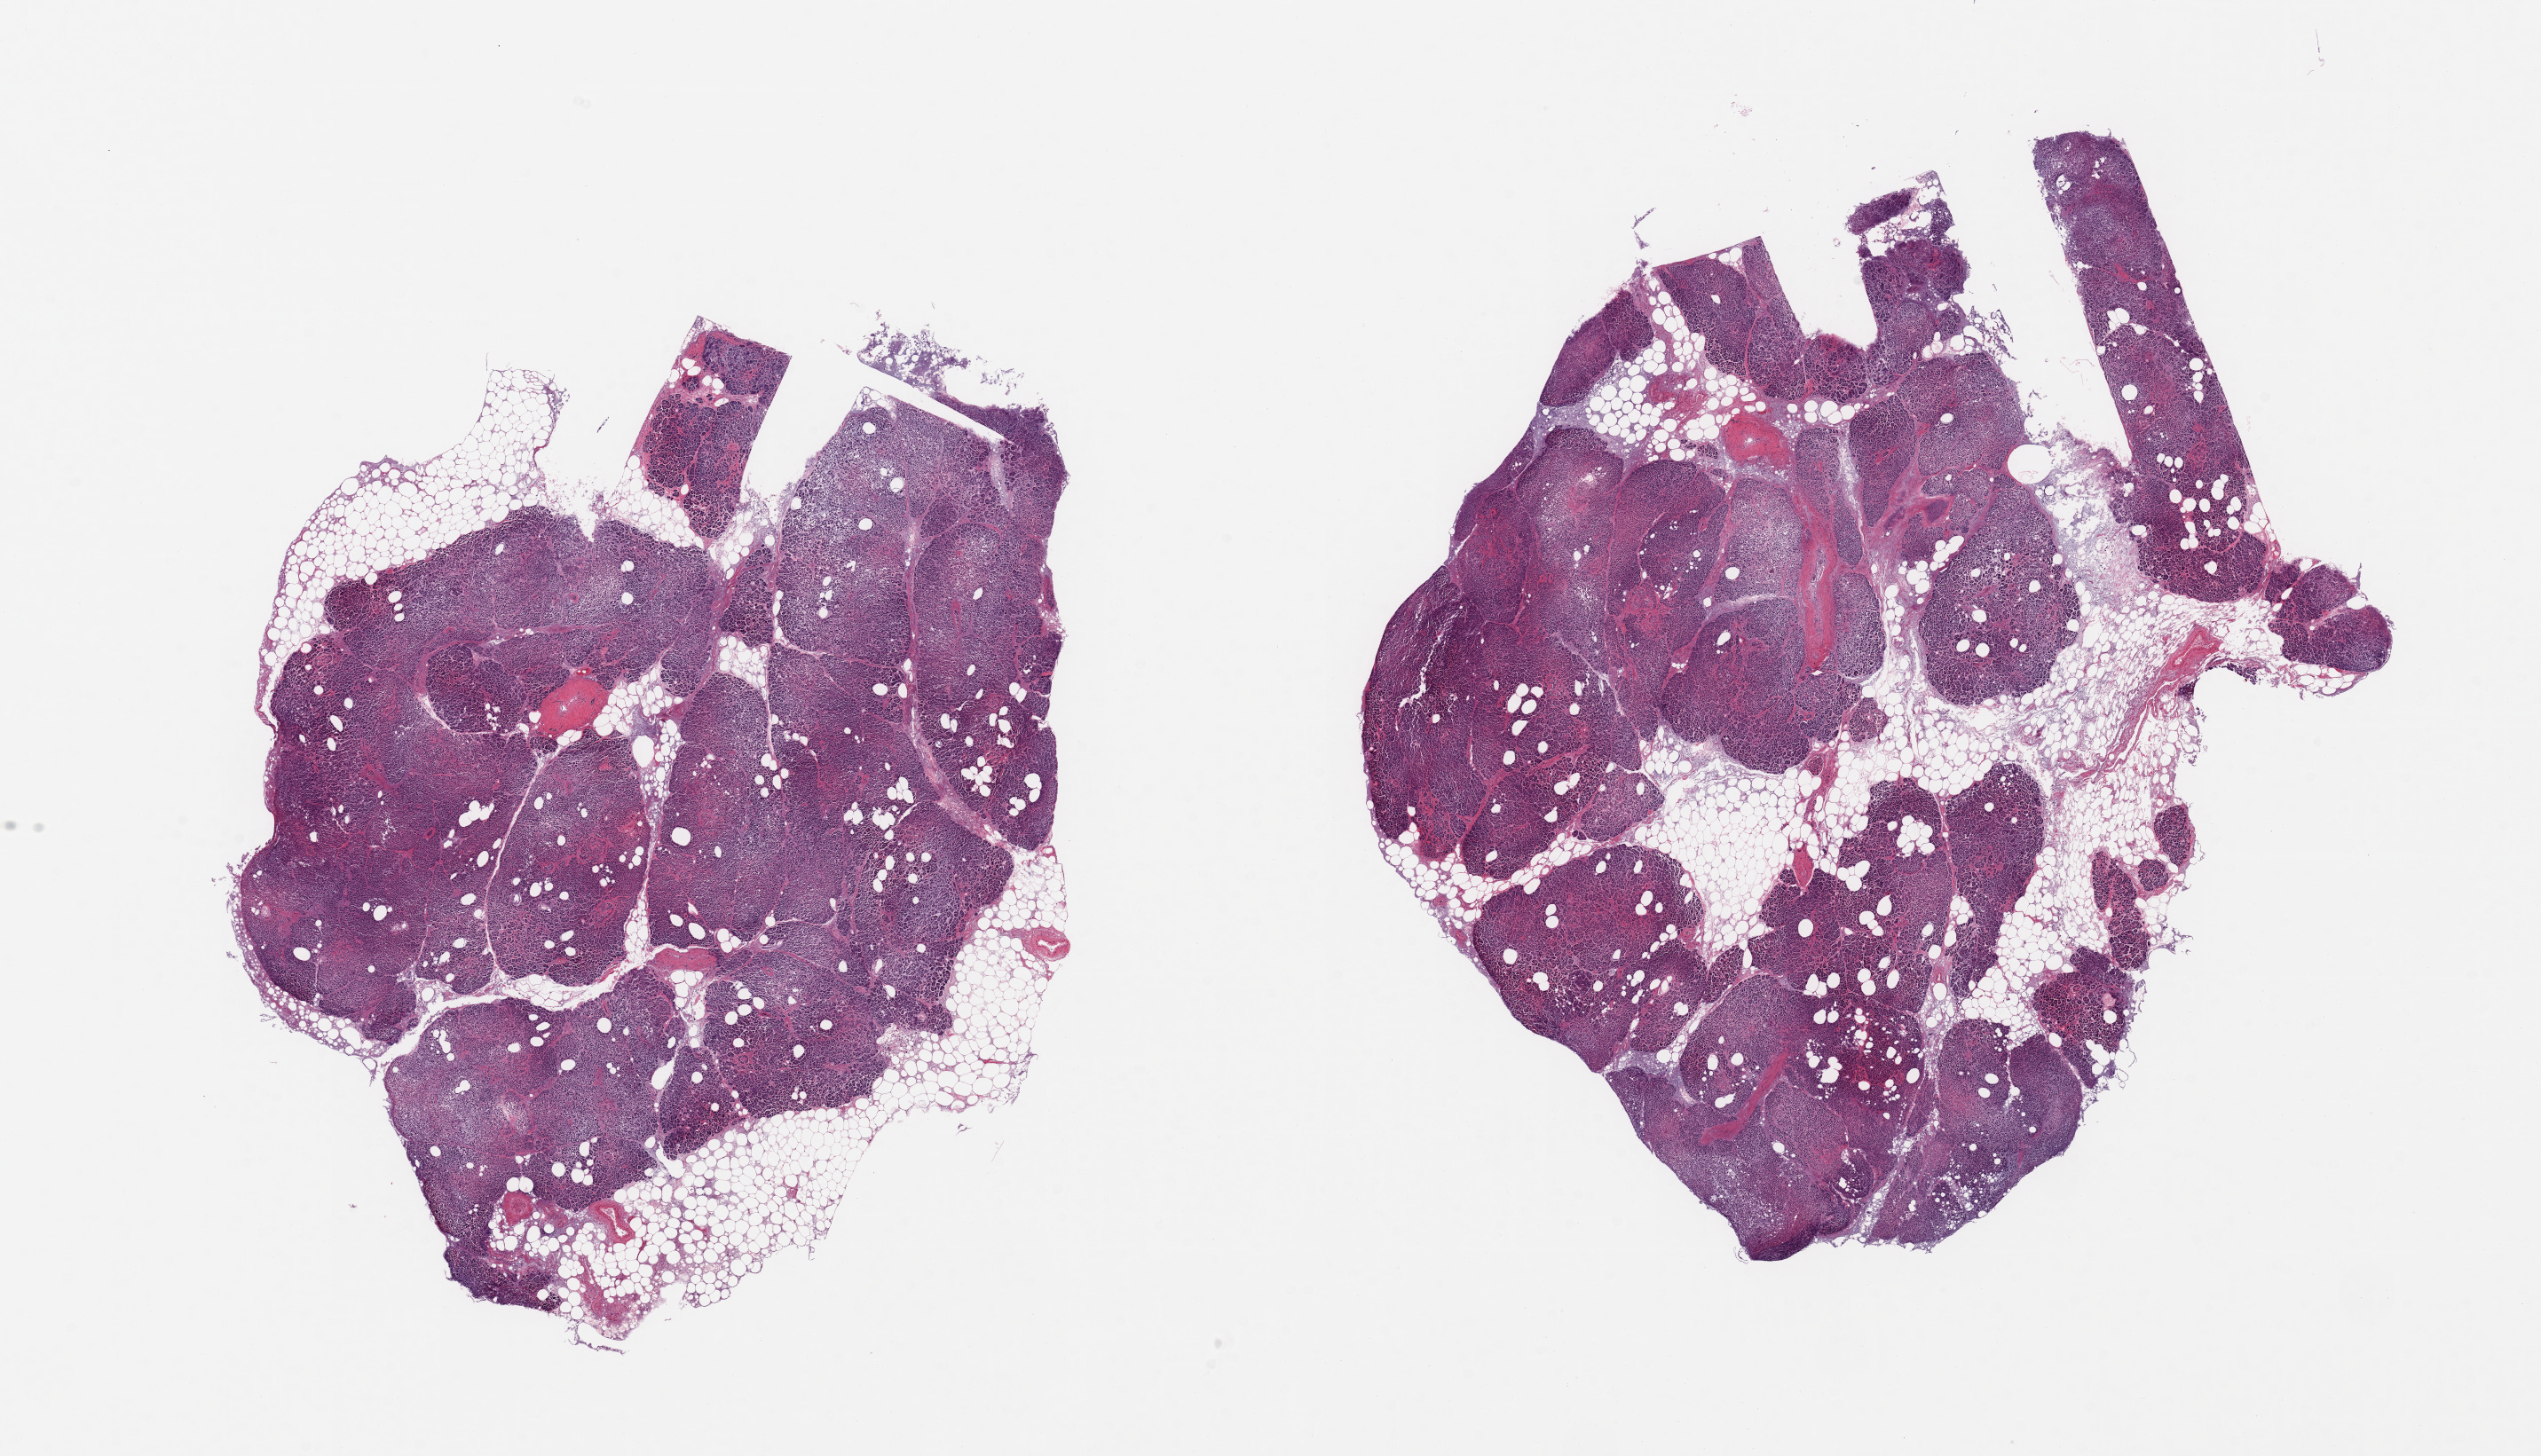
Whole-slide image, H&E stain — shown as a low-resolution overview of the whole scanned area (about 22.6 x 13.0 mm, slide scanned at 20x), PAXgene-fixed, paraffin-embedded tissue, sampled site (target tissue): pancreas, tissue donor sample. Donor sex: female.
Reviewer comment on this tissue sample: 2 pieces, moderate-advanced saponification, Islets not visible.